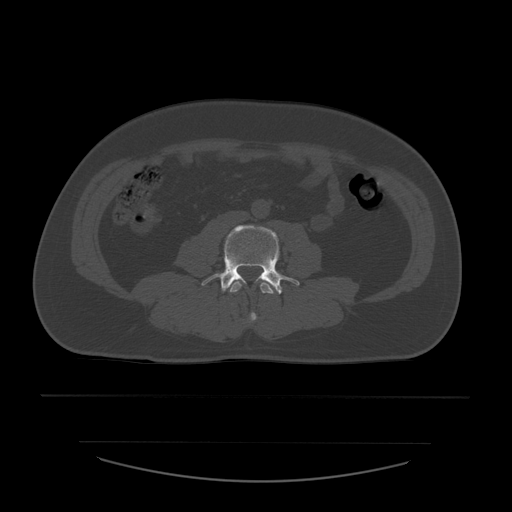
CT including the spine, one axial slice. Position 154 of 532 along the scan axis. 120 kVp. Bone window (W 1800 / L 400 HU). 1.25 mm slice thickness. 512 × 512 image matrix. Patient age 44 years. From the clinical record (not read from this slice): primary cancer: soft tissue sarcoma.
Annotated regions visible in this slice (semi-automatically segmented with operator editing):
- L3 vertebra: bounding box <230,281,276,322> (left, top, right, bottom; pixels)
- L4 vertebra: <202,225,300,295>